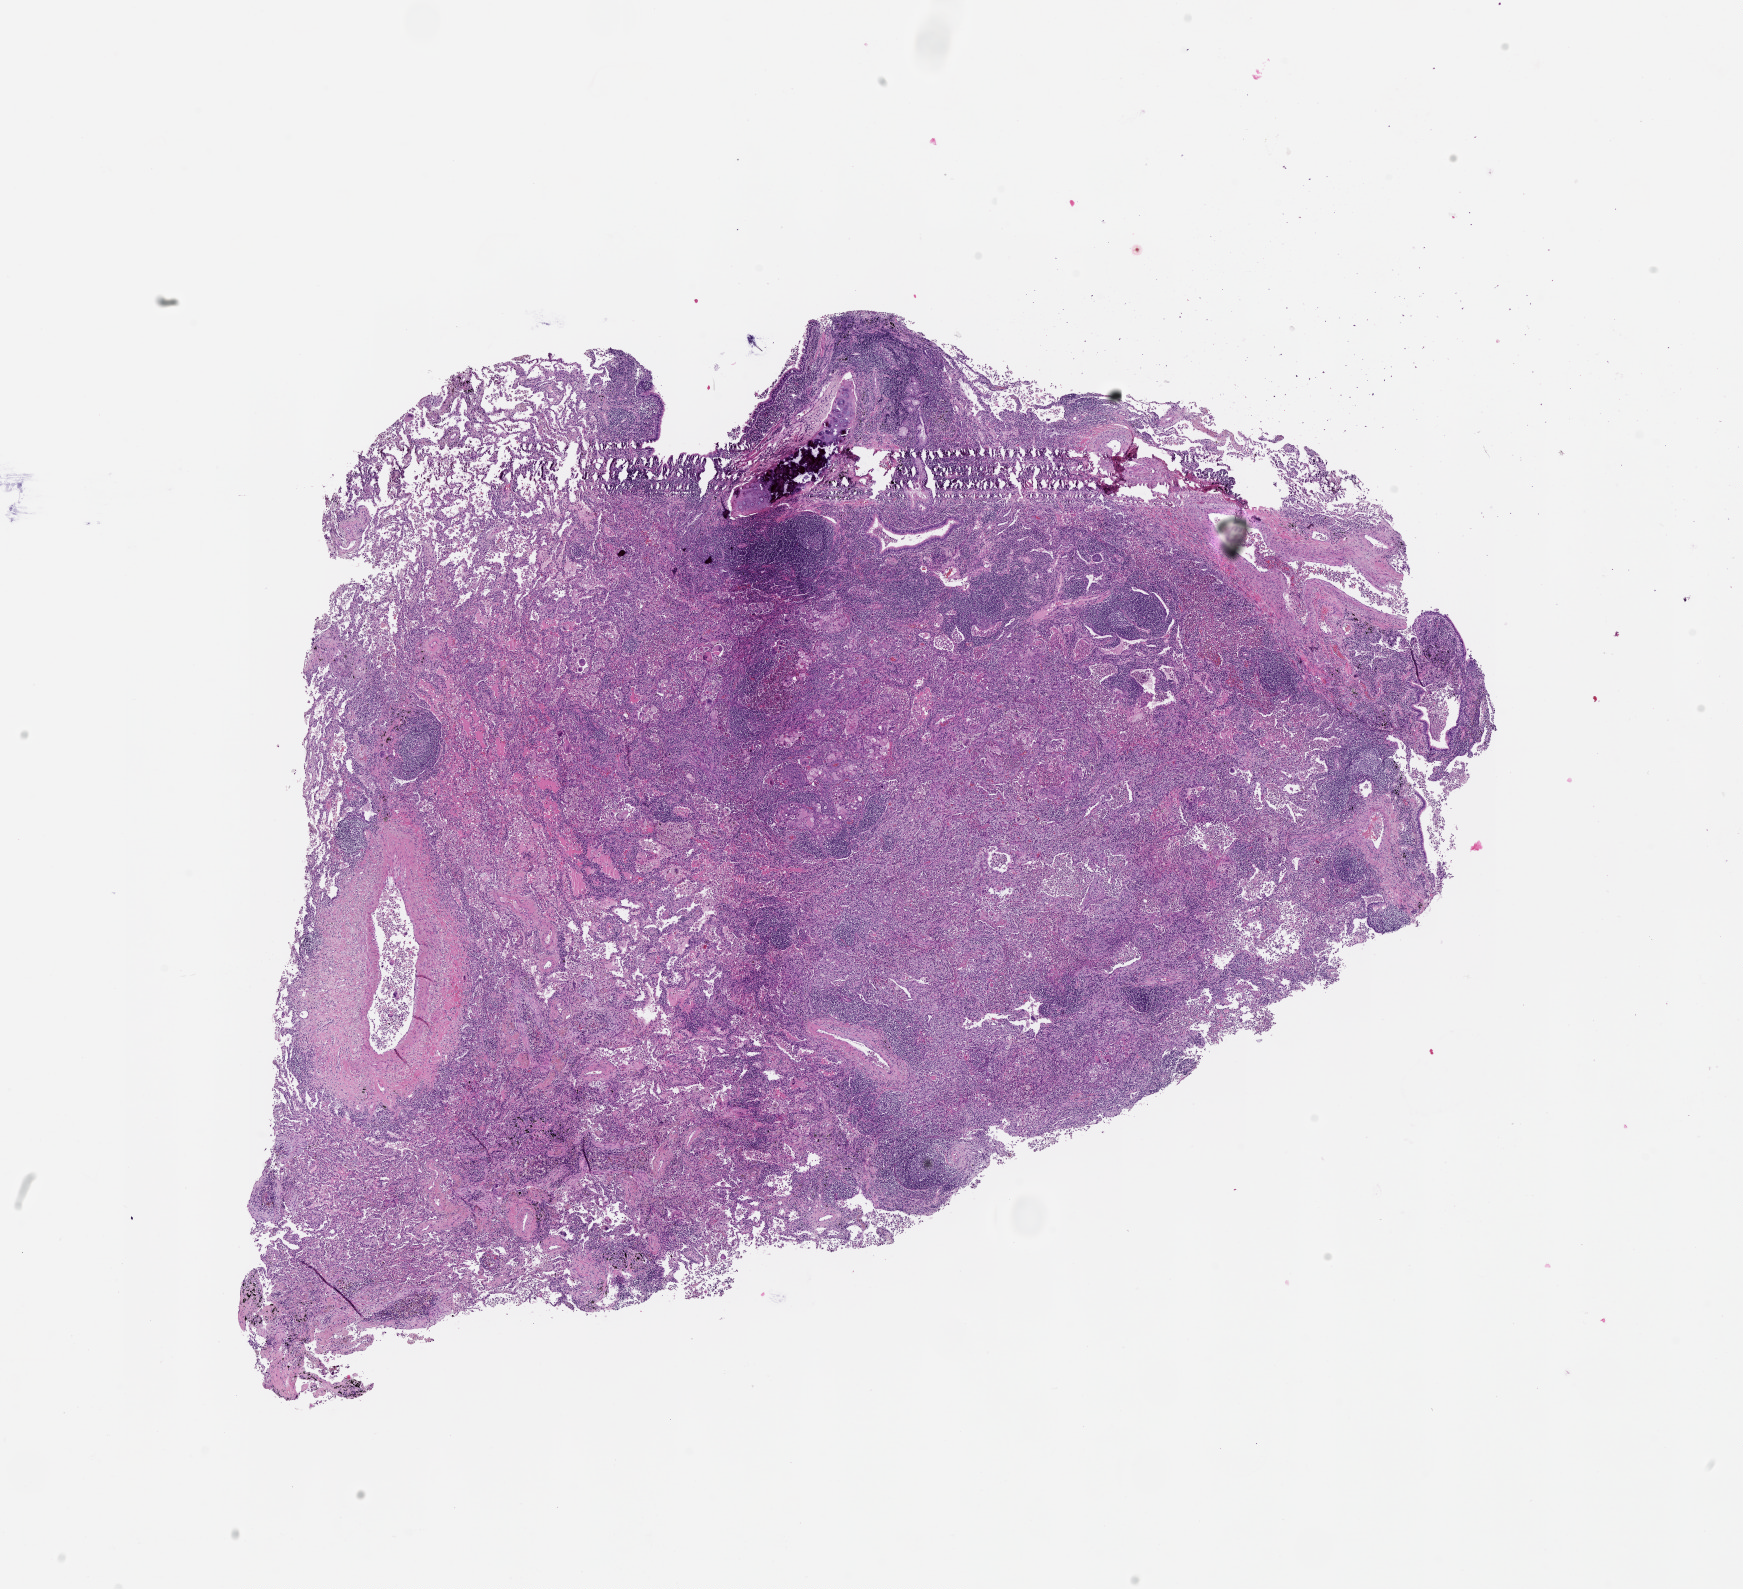
H&E whole-slide image — a low-resolution overview of the entire scanned area, about 14.0 x 12.8 mm; tumour tissue sample, lung. Male, 64 y/o.
* patient diagnosis (cohort enrolment): squamous cell carcinoma (lung)